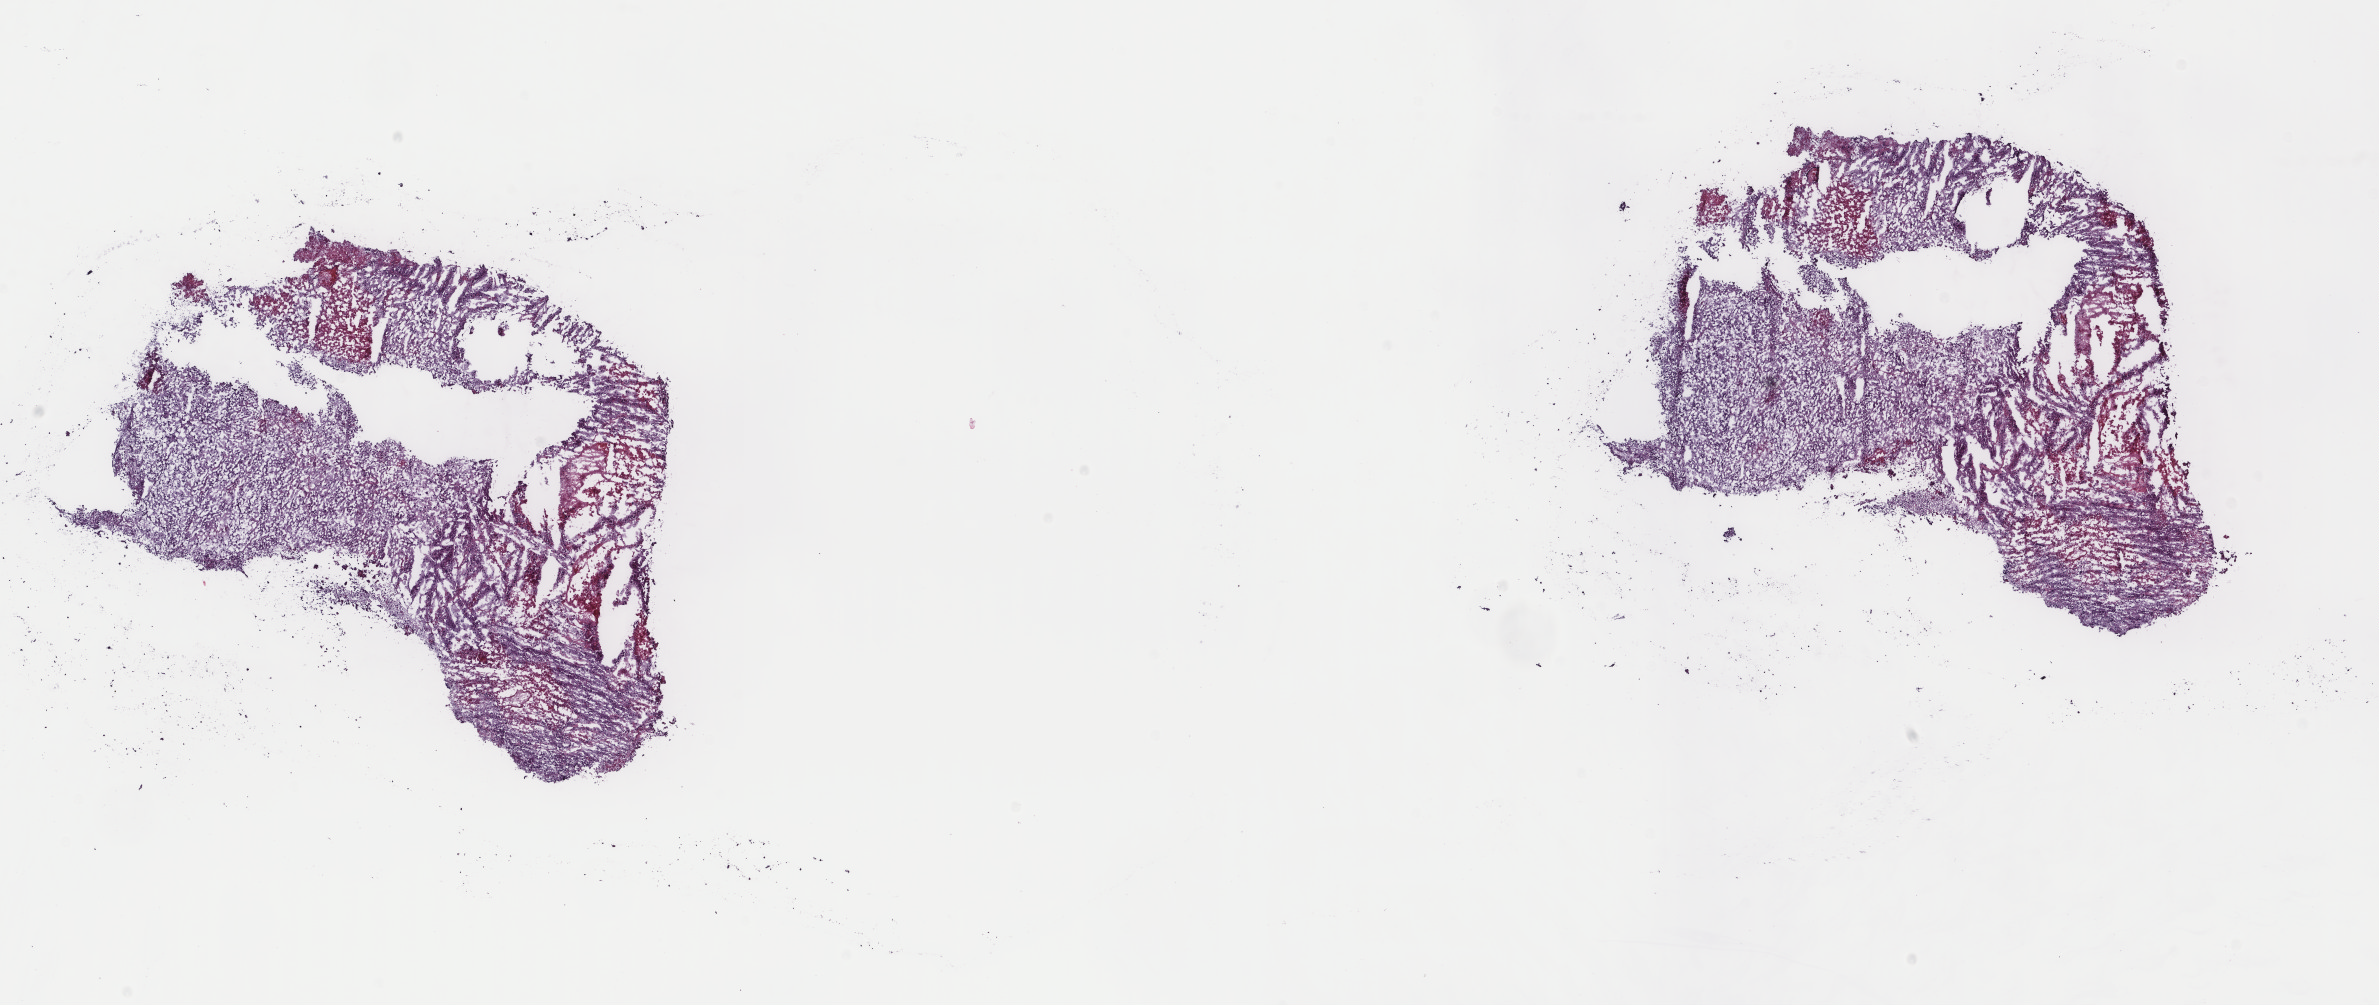
Hematoxylin and eosin (H&E) stained whole-slide image, whole scanned area (about 18.9 x 8.0 mm) shown as a low-resolution overview. Frozen section from the top of the tissue portion. Adrenal cortex, primary tumour sample. Patient: female, age at initial diagnosis 68 years. Pathologist review of this section (percent, as recorded): tumour cells 80%, tumour nuclei 90%, normal cells 0%, stromal cells 0%, necrosis 20%. Inflammatory infiltration, as recorded: lymphocyte infiltration 0%, monocyte infiltration 0%, neutrophil infiltration 0%.
* histologic diagnosis: Adrenal cortical carcinoma (cortex of adrenal gland)